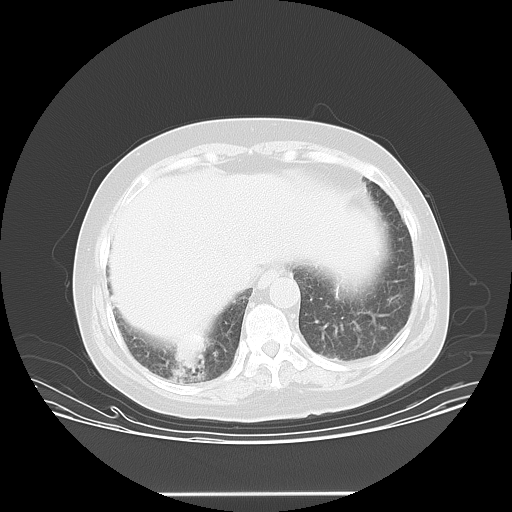
Chest CT, one axial slice. Slice 6 of 45 in the series (ordered by position). Reconstruction kernel LUNG. Lung window (W 1500 / L -600 HU). 5 mm slice thickness. 512 × 512 image matrix, field of view 408 × 408 mm. Female patient, age 55 years. From the clinical record (not read from this slice): clinical TNM (as recorded): T2 N0 M1b.
Structures marked on this image (bounding box drawn by a radiologist):
- lung tumour (recorded histology: squamous cell carcinoma): bounding box <162,336,214,392> (left, top, right, bottom; pixels)